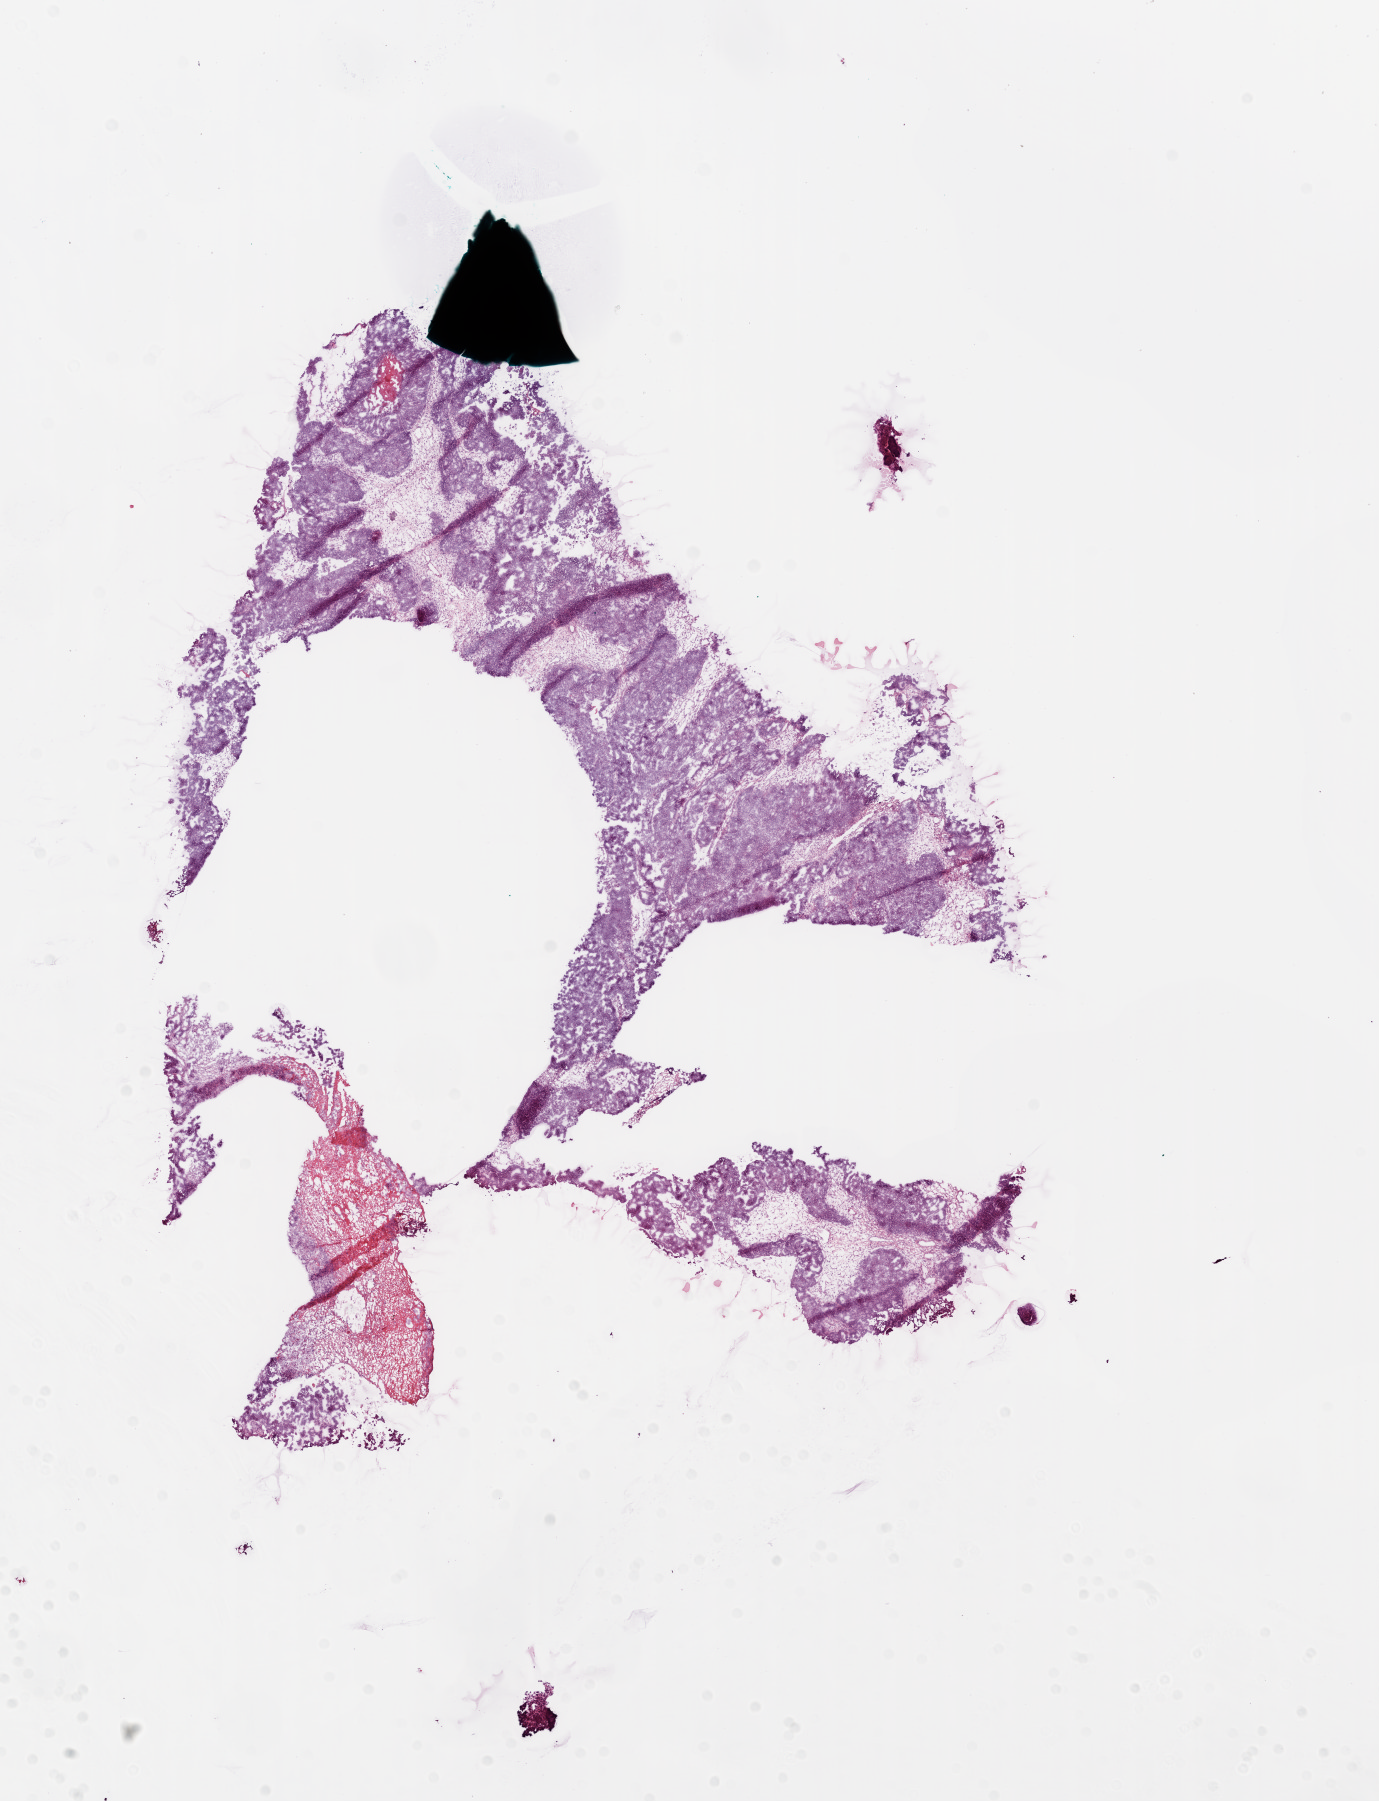
H&E-stained whole-slide image — a low-resolution overview of the entire scanned area, about 11.1 x 14.5 mm. Frozen section from the bottom of the tissue portion. Ovary, primary tumour sample. Female, age 44 years at initial diagnosis. Histologic grade: G3 (poorly differentiated). Composition of this section per pathologist review: tumour cells 80%, tumour nuclei 85%, normal cells 5%, stromal cells 15%, necrosis 0%.
Diagnosis: Serous cystadenocarcinoma, NOS. FIGO stage: IIIC.